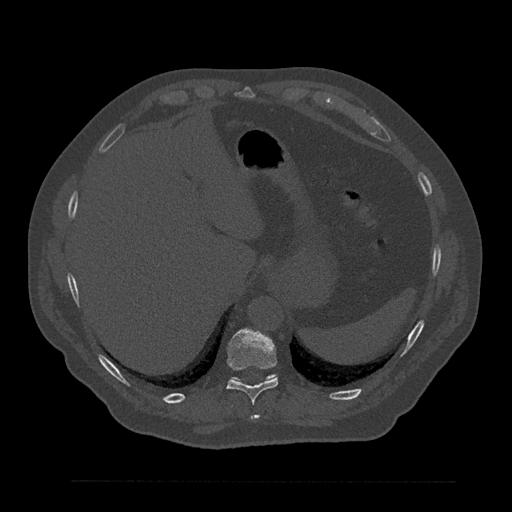
CT including the spine, one axial slice; position 338 of 797 along the scan axis; reconstruction kernel Br40s/3; bone window (W 1800 / L 400 HU); 512 × 512 image matrix, field of view 430 × 430 mm. Male patient, age 61 years. Case-level facts recorded for this patient, not image findings: primary cancer: prostate.
Annotated regions visible in this slice (semi-automatically segmented with operator editing):
- T10 vertebra: bounding box [x1, y1, x2, y2] px = [227, 329, 278, 404]
- T11 vertebra: [231, 374, 275, 381]
- T9 vertebra: [250, 415, 259, 420]